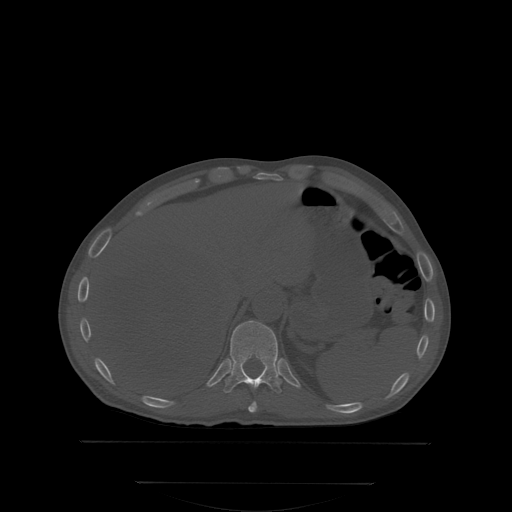
CT including the spine, one axial slice. Position 182 of 350 along the scan axis. Bone window (W 1800 / L 400 HU). 2.5 mm slice thickness. 512 × 512 image matrix. Male patient, age 58 years. Case-level facts recorded for this patient, not image findings: primary cancer: prostate; vertebrae with lytic lesions (as recorded): L1.
Structures marked on this image (semi-automatically segmented with operator editing):
- T10 vertebra: bounding box (x1, y1, x2, y2) in pixels: (249, 401, 257, 411)
- T11 vertebra: (223, 320, 292, 393)